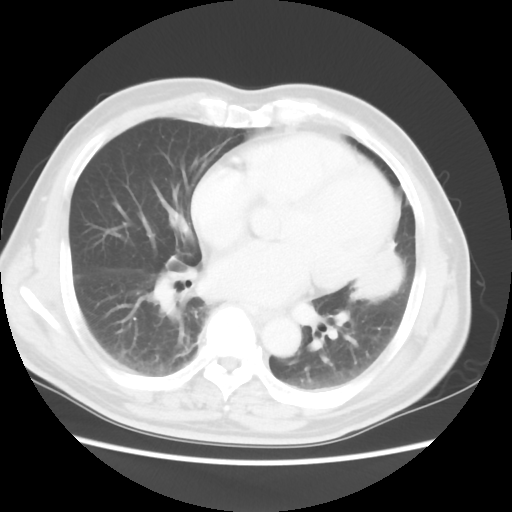
Chest CT, one axial slice; slice 21 of 50 in the series (ordered by position); reconstruction kernel STANDARD; lung window (W 1500 / L -600 HU); 5 mm slice thickness; 512 × 512 image matrix. Patient: male, 69 years. Case-level facts recorded for this patient, not image findings: clinical TNM (as recorded): T3 N1 M1a.
Structures marked on this image (bounding box drawn by a radiologist):
- lung tumour (recorded histology: squamous cell carcinoma): bounding box (x1, y1, x2, y2) in pixels: (342, 233, 409, 303)